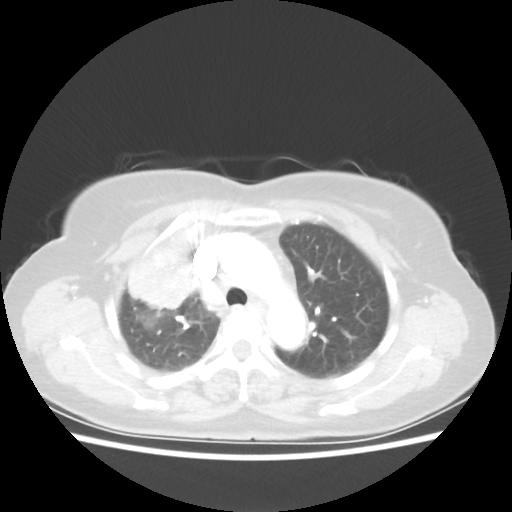
Chest CT, one axial slice; position 39 of 55 along the scan axis; reconstruction kernel STANDARD; 80 kVp; lung window (W 1500 / L -600 HU); 5 mm slice thickness; 512 × 512 image matrix. Patient: female, 62 years. Case-level facts recorded for this patient, not image findings: clinical TNM (as recorded): T4 N3 M0.
Structures marked on this image (bounding box drawn by a radiologist):
- lung tumour (recorded histology: squamous cell carcinoma): bounding box (x1, y1, x2, y2) in pixels: (120, 231, 214, 316)